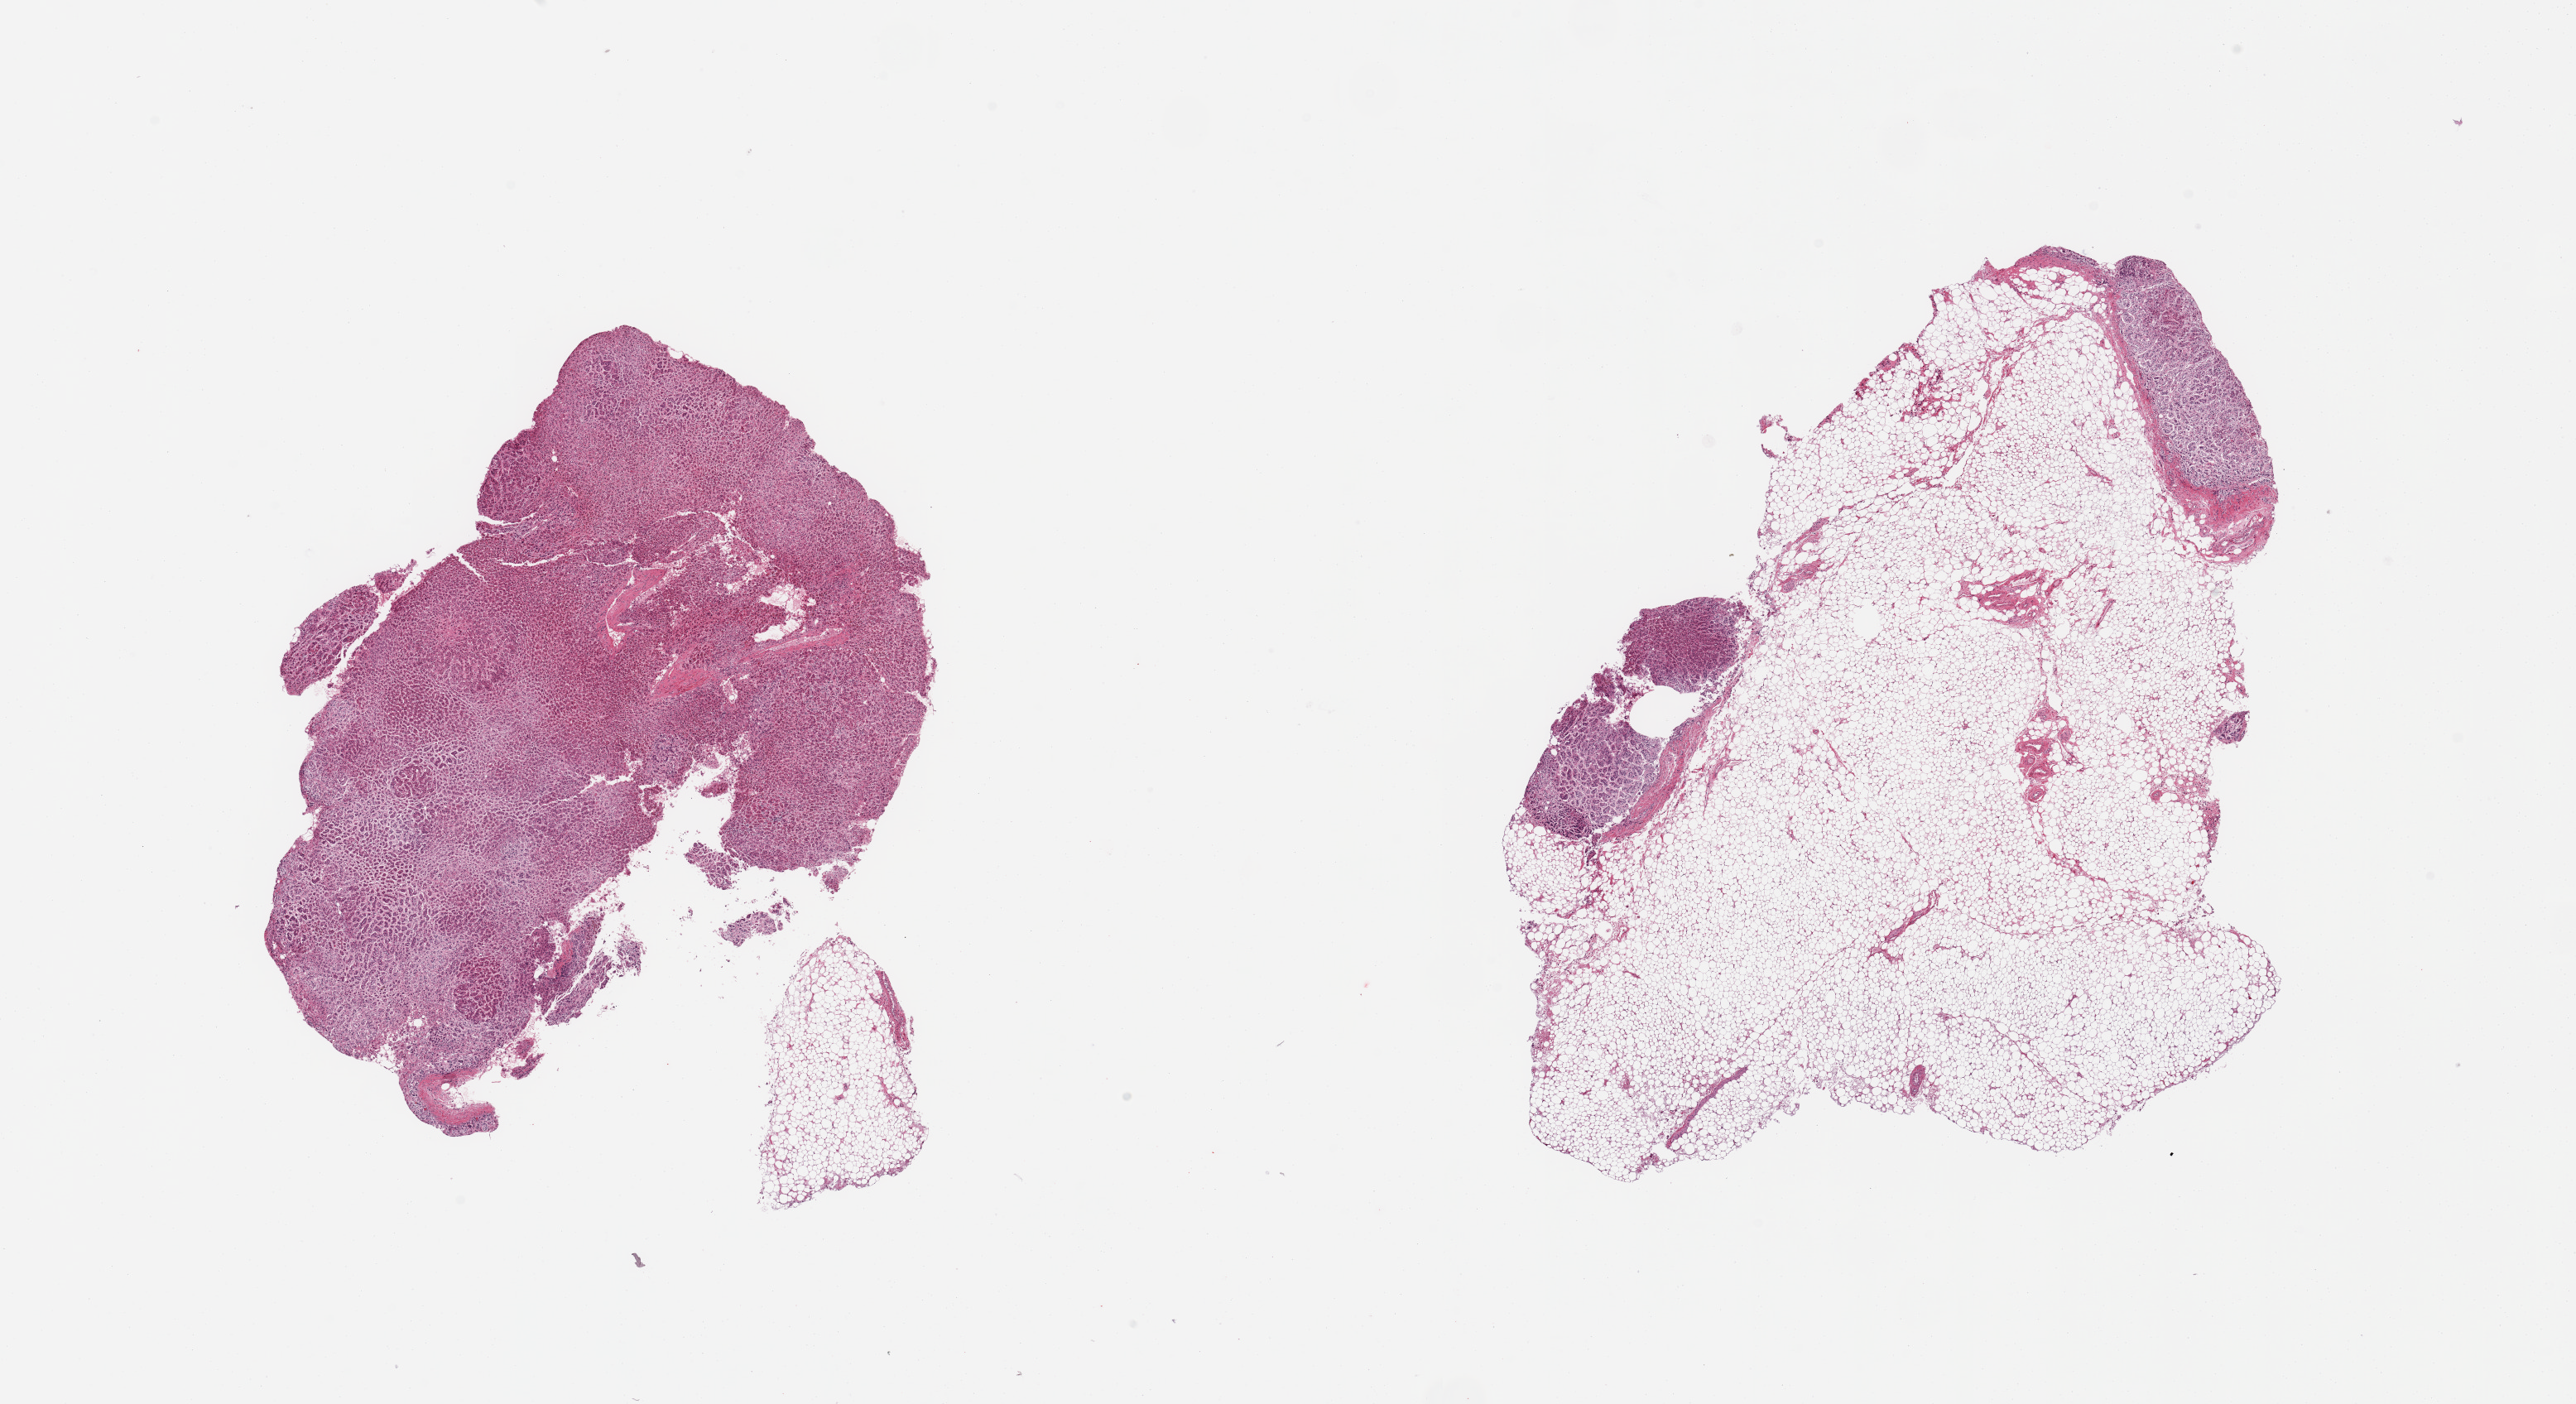
Hematoxylin and eosin (H&E) whole-slide image — whole scanned area (about 24.6 x 13.4 mm) shown as a low-resolution overview, PAXgene-fixed, paraffin-embedded tissue, target tissue: adrenal gland, donor tissue sample. Male donor.
- pathologist's review note for this sample: 2 pieces: 1 with 80% fat